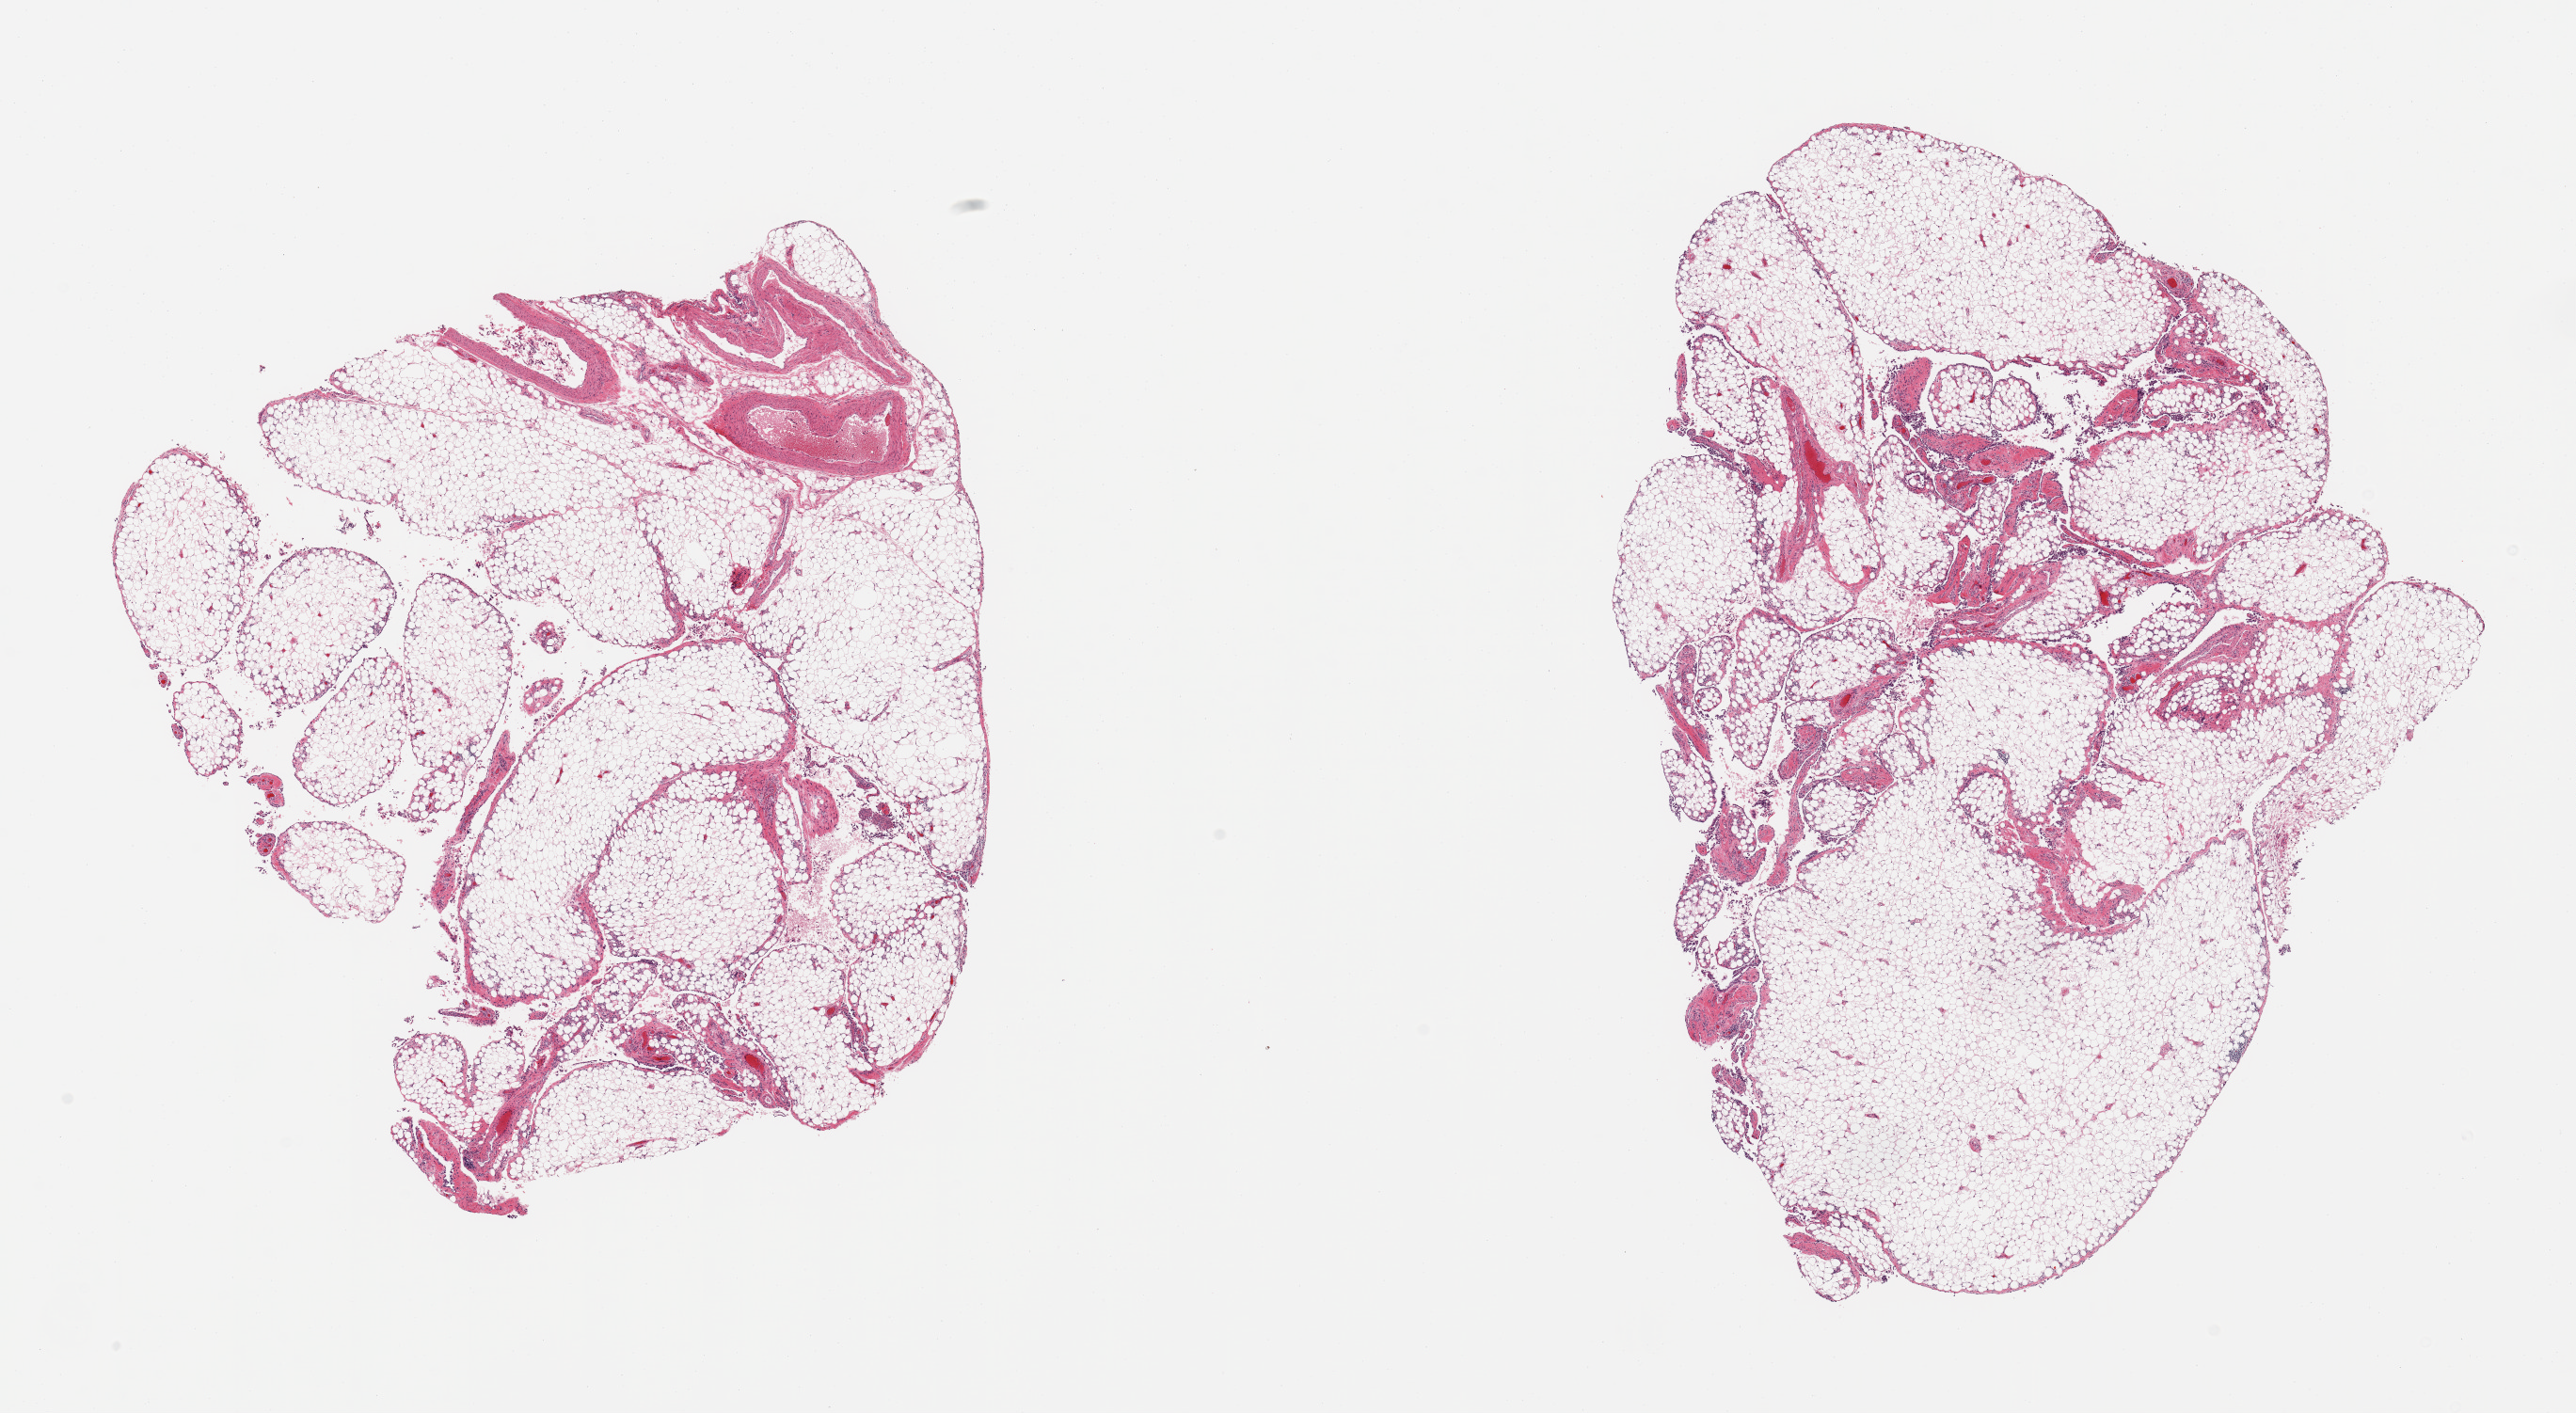
Whole-slide image, hematoxylin and eosin (H&E) stain — whole scanned area (about 21.7 x 11.9 mm, from a 20x scan) shown as a low-resolution overview, PAXgene-fixed paraffin-embedded (PFPE) section, section of omentum (target tissue), donor tissue sample. Male donor.
Pathologist's review note for this sample: 2 pieces, fascia, prominent vascular elements are ~20% tissue total.